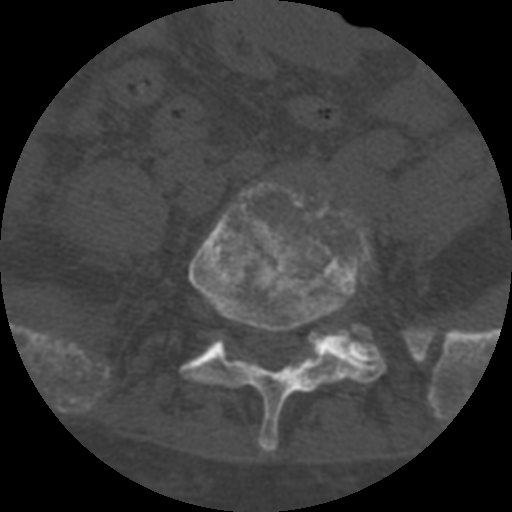
CT including the spine, one axial slice; slice 181 of 708 in the series (ordered by position); 120 kVp; one of 3 acquisitions stored at this slice position; bone window (W 1800 / L 400 HU); 1.25 mm slice thickness; 512 × 512 image matrix, field of view 160 × 160 mm. Patient age 55 years. From the clinical record (not read from this slice): primary cancer: colon; vertebrae with lytic lesions (as recorded): T12, L1, L5.
Outlined on this slice (semi-automatic segmentation, software-assisted and operator-edited):
- L5 vertebra: bounding box <182,182,387,453> (left, top, right, bottom; pixels)